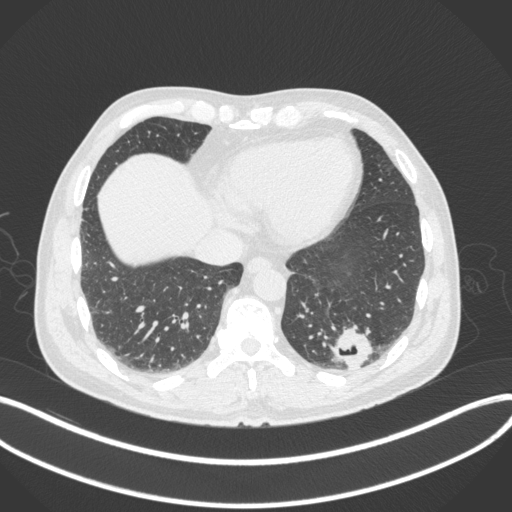
Chest CT, one axial slice. Slice 73 of 313 in the series (ordered by position). Reconstruction kernel B31f. 120 kVp. Lung window (W 1500 / L -600 HU). 1 mm slice thickness. 512 × 512 image matrix. Male patient, age 54 years. Case-level facts recorded for this patient, not image findings: clinical TNM (as recorded): T1c N0 M1; histopathological grade: G3.
Structures marked on this image (bounding box drawn by a radiologist):
- lung tumour (recorded histology: adenocarcinoma): box from (x=327, y=325) to (x=373, y=371) px